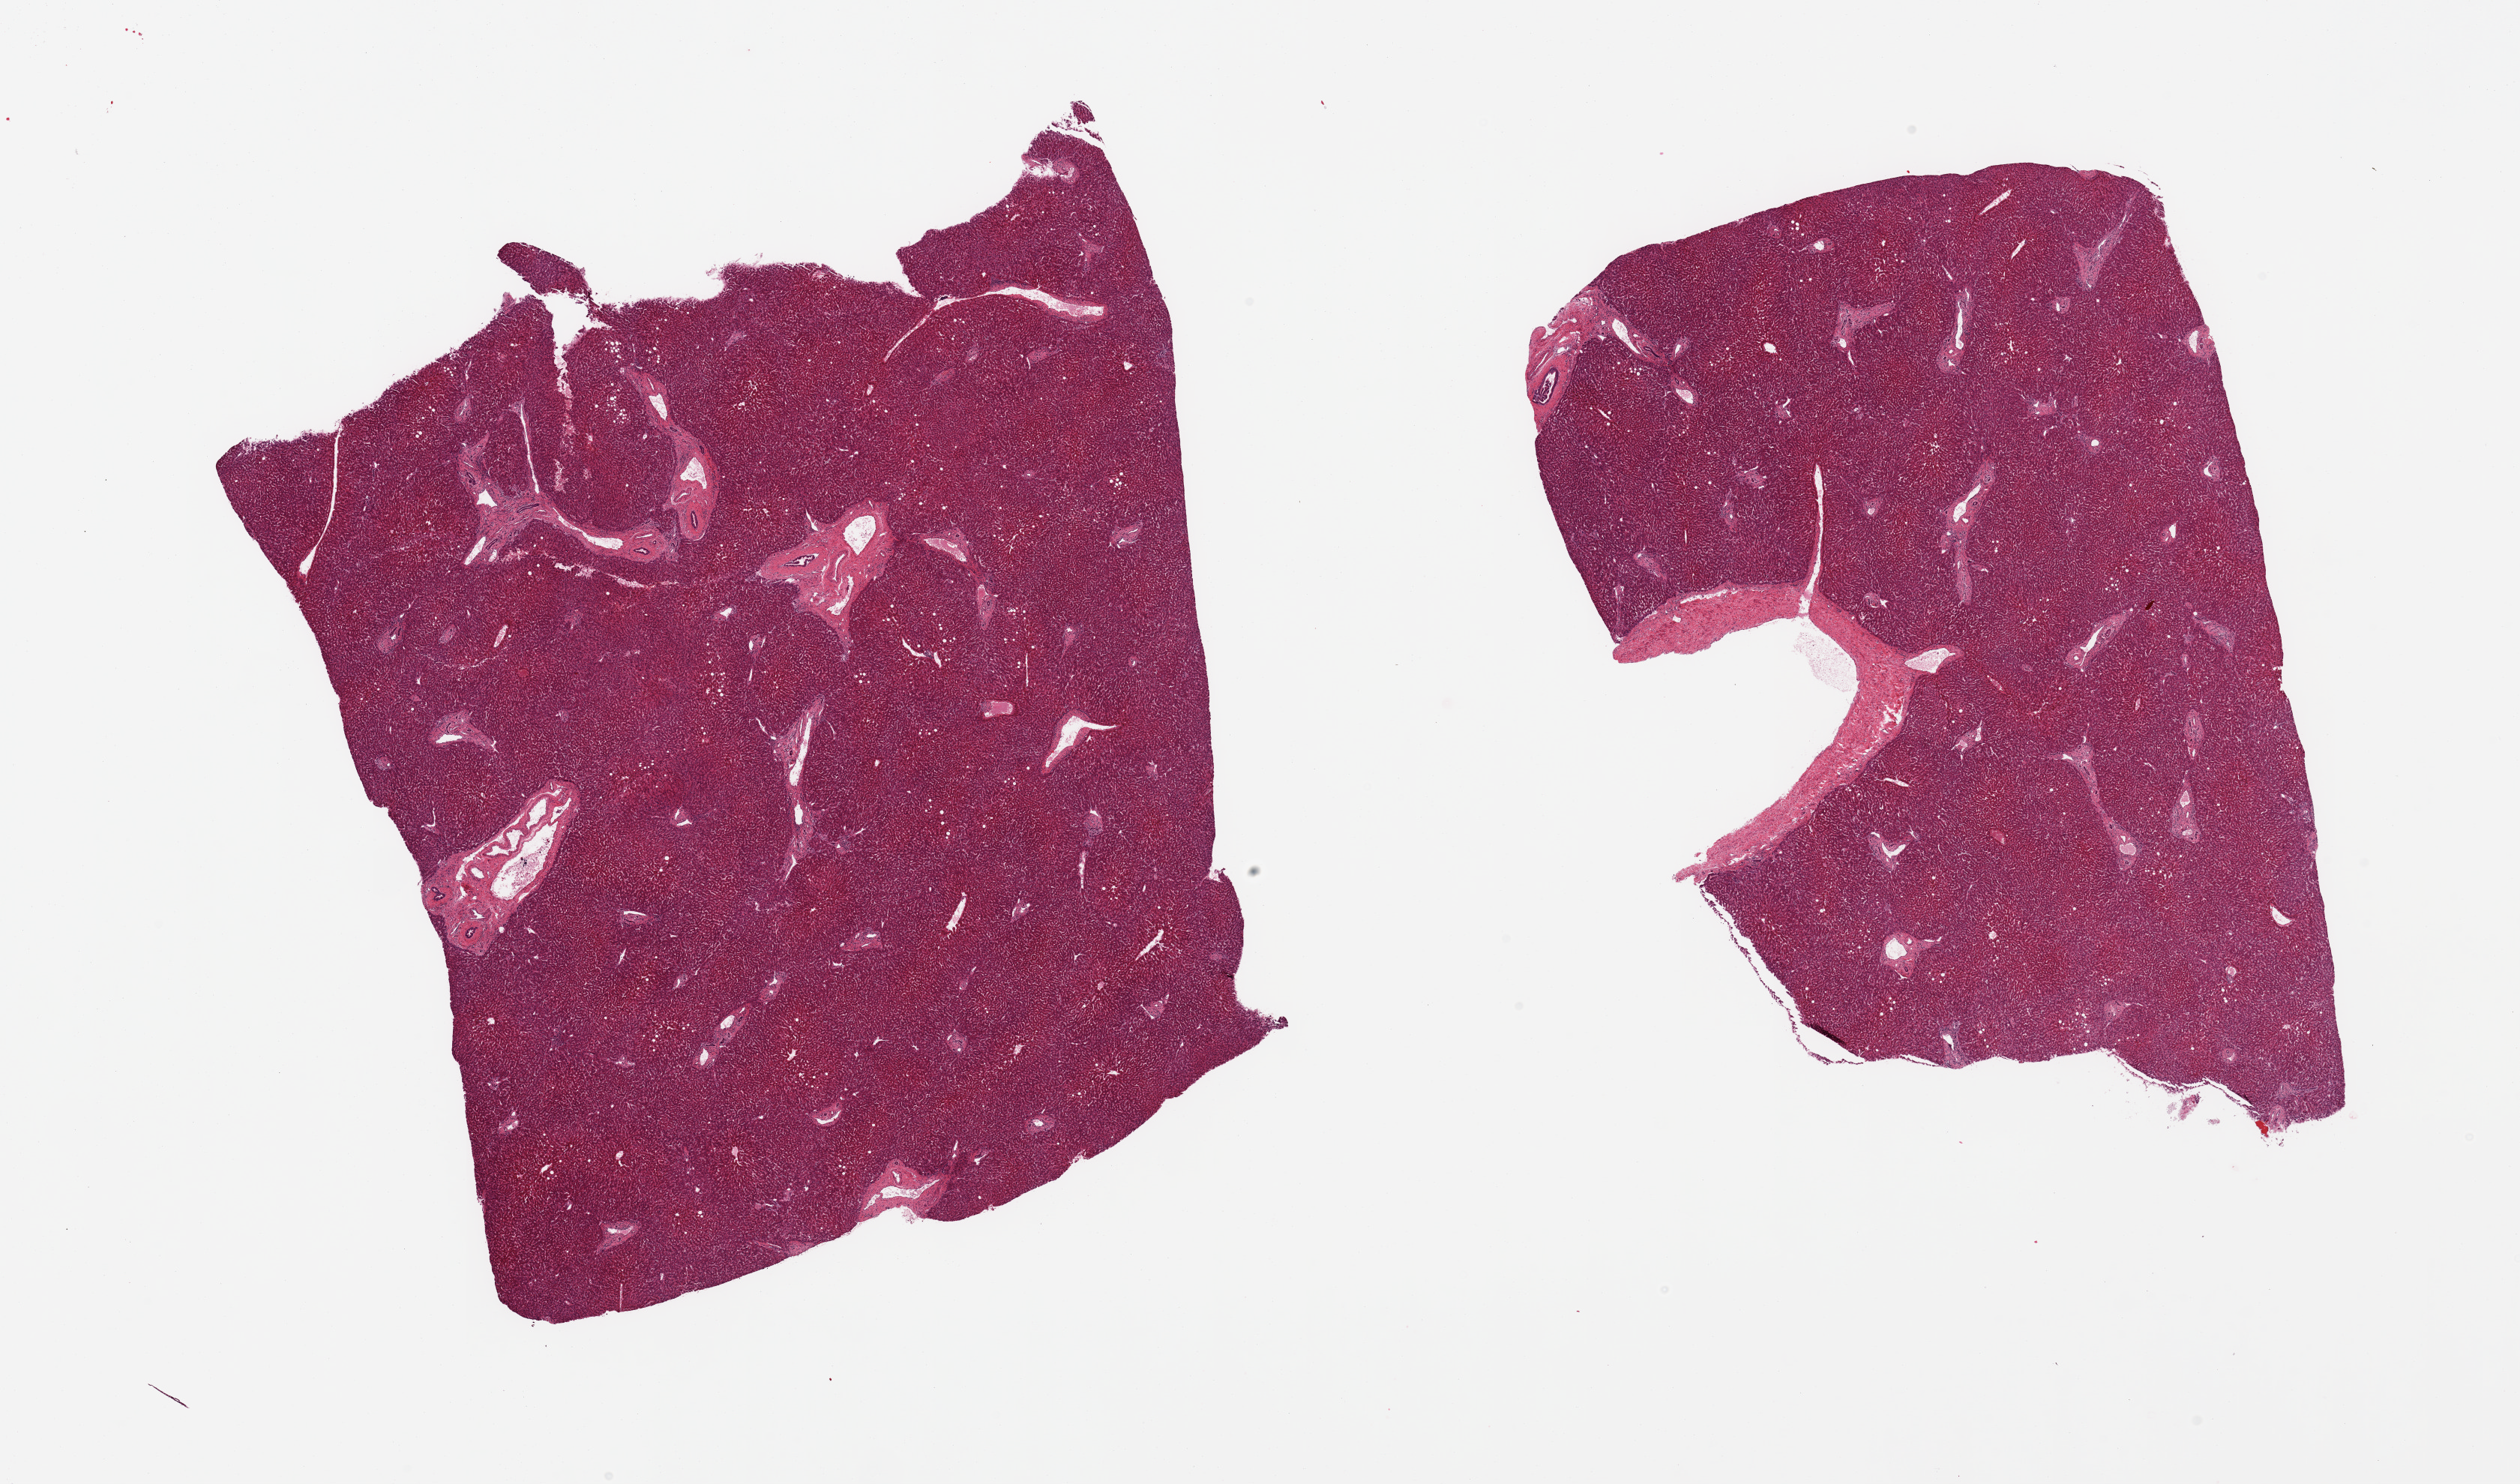
Whole-slide image, hematoxylin and eosin (H&E) stain, whole scanned area (about 26.6 x 15.7 mm, slide scanned at 20x) shown as a low-resolution overview. PAXgene-fixed paraffin-embedded (PFPE) section. Target tissue: liver. Donor tissue sample. Female donor.
- review note (as recorded): 2 pieces, no significant steatosis or hepatitis